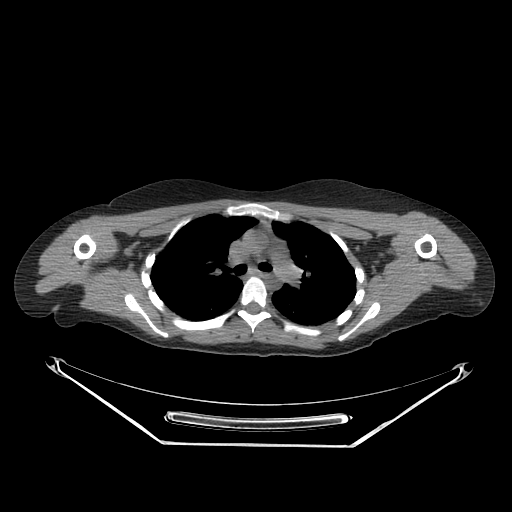
CT of an extremity soft-tissue mass (from a PET/CT study), one axial slice; slice 200 of 267 in the series (ordered by position); reconstruction kernel SOFT; 140 kVp; soft-tissue window (W 400 / L 40 HU); 512 × 512 image matrix, field of view 500 × 500 mm. Female patient. Case-level facts recorded for this patient, not image findings: histological type: malignant fibrous histiocytoma; grade: low; site of the primary tumour: left arm.
Outlined on this slice (expert contour drawn on MRI and transferred to this co-registered scan by the dataset authors):
- gross tumour volume (mass): bounding box <436,258,455,277> (left, top, right, bottom; pixels)